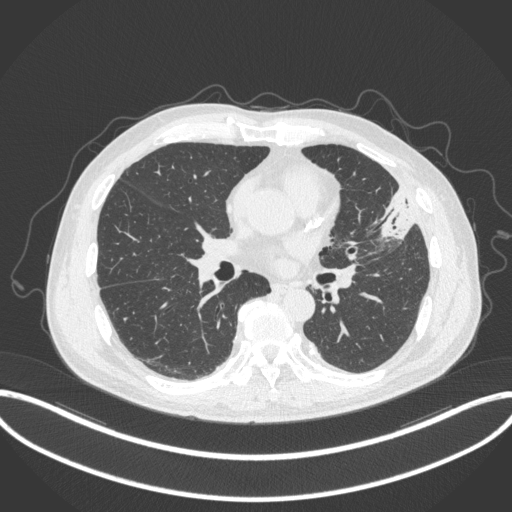
Chest CT, one axial slice; slice 165 of 382 in the series (ordered by position); reconstruction kernel B31f; 120 kVp; lung window (W 1500 / L -600 HU); 1 mm slice thickness; 512 × 512 image matrix. Patient: male, 64 years. Case-level facts recorded for this patient, not image findings: clinical TNM (as recorded): T4 N1 M0.
Outlined on this slice (bounding box drawn by a radiologist):
- lung tumour (recorded histology: adenocarcinoma): box from (x=372, y=182) to (x=422, y=243) px